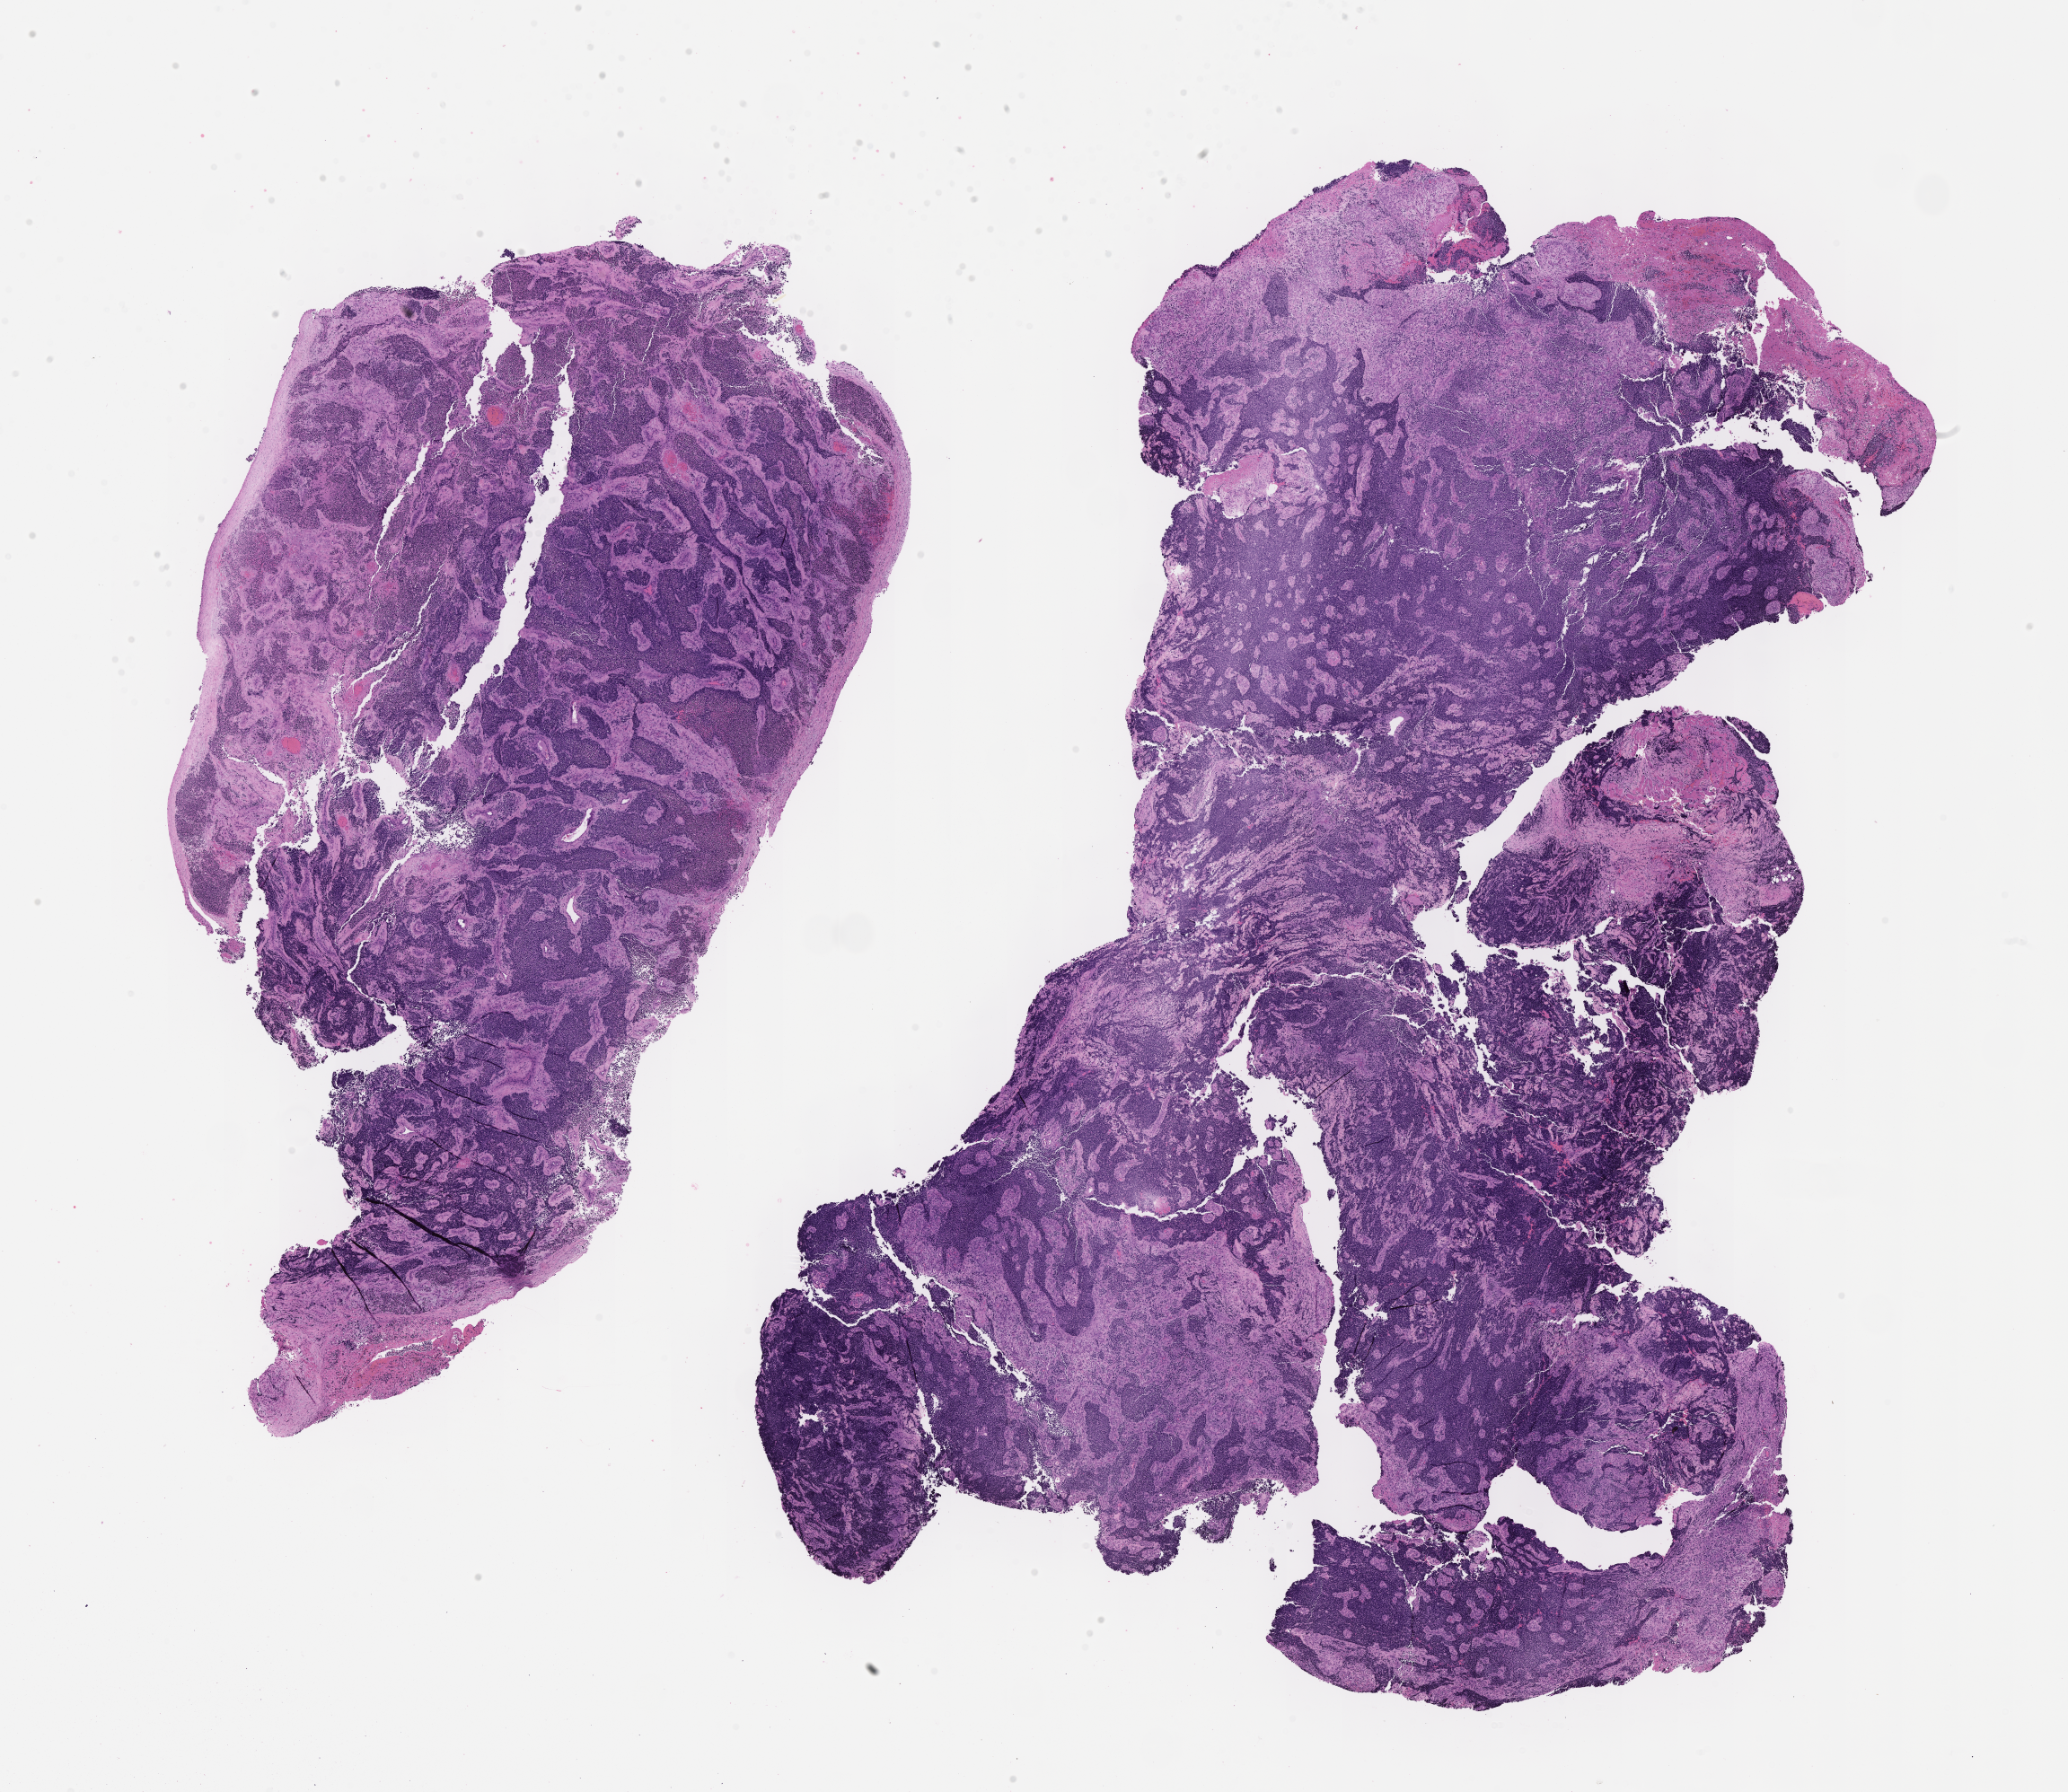
Hematoxylin and eosin (H&E) whole-slide image of tumor tissue — shown as a low-resolution overview of the whole scanned area (about 18.6 x 16.1 mm), formalin-fixed, paraffin-embedded (FFPE) tissue, sample anatomic site: chest, left. Male patient, age at diagnosis 17.7 years.
* stage (as recorded): 4
* primary site (case record): pleura
* diagnosis: rhabdomyosarcoma; histological classification: alveolar rhabdomyosarcoma